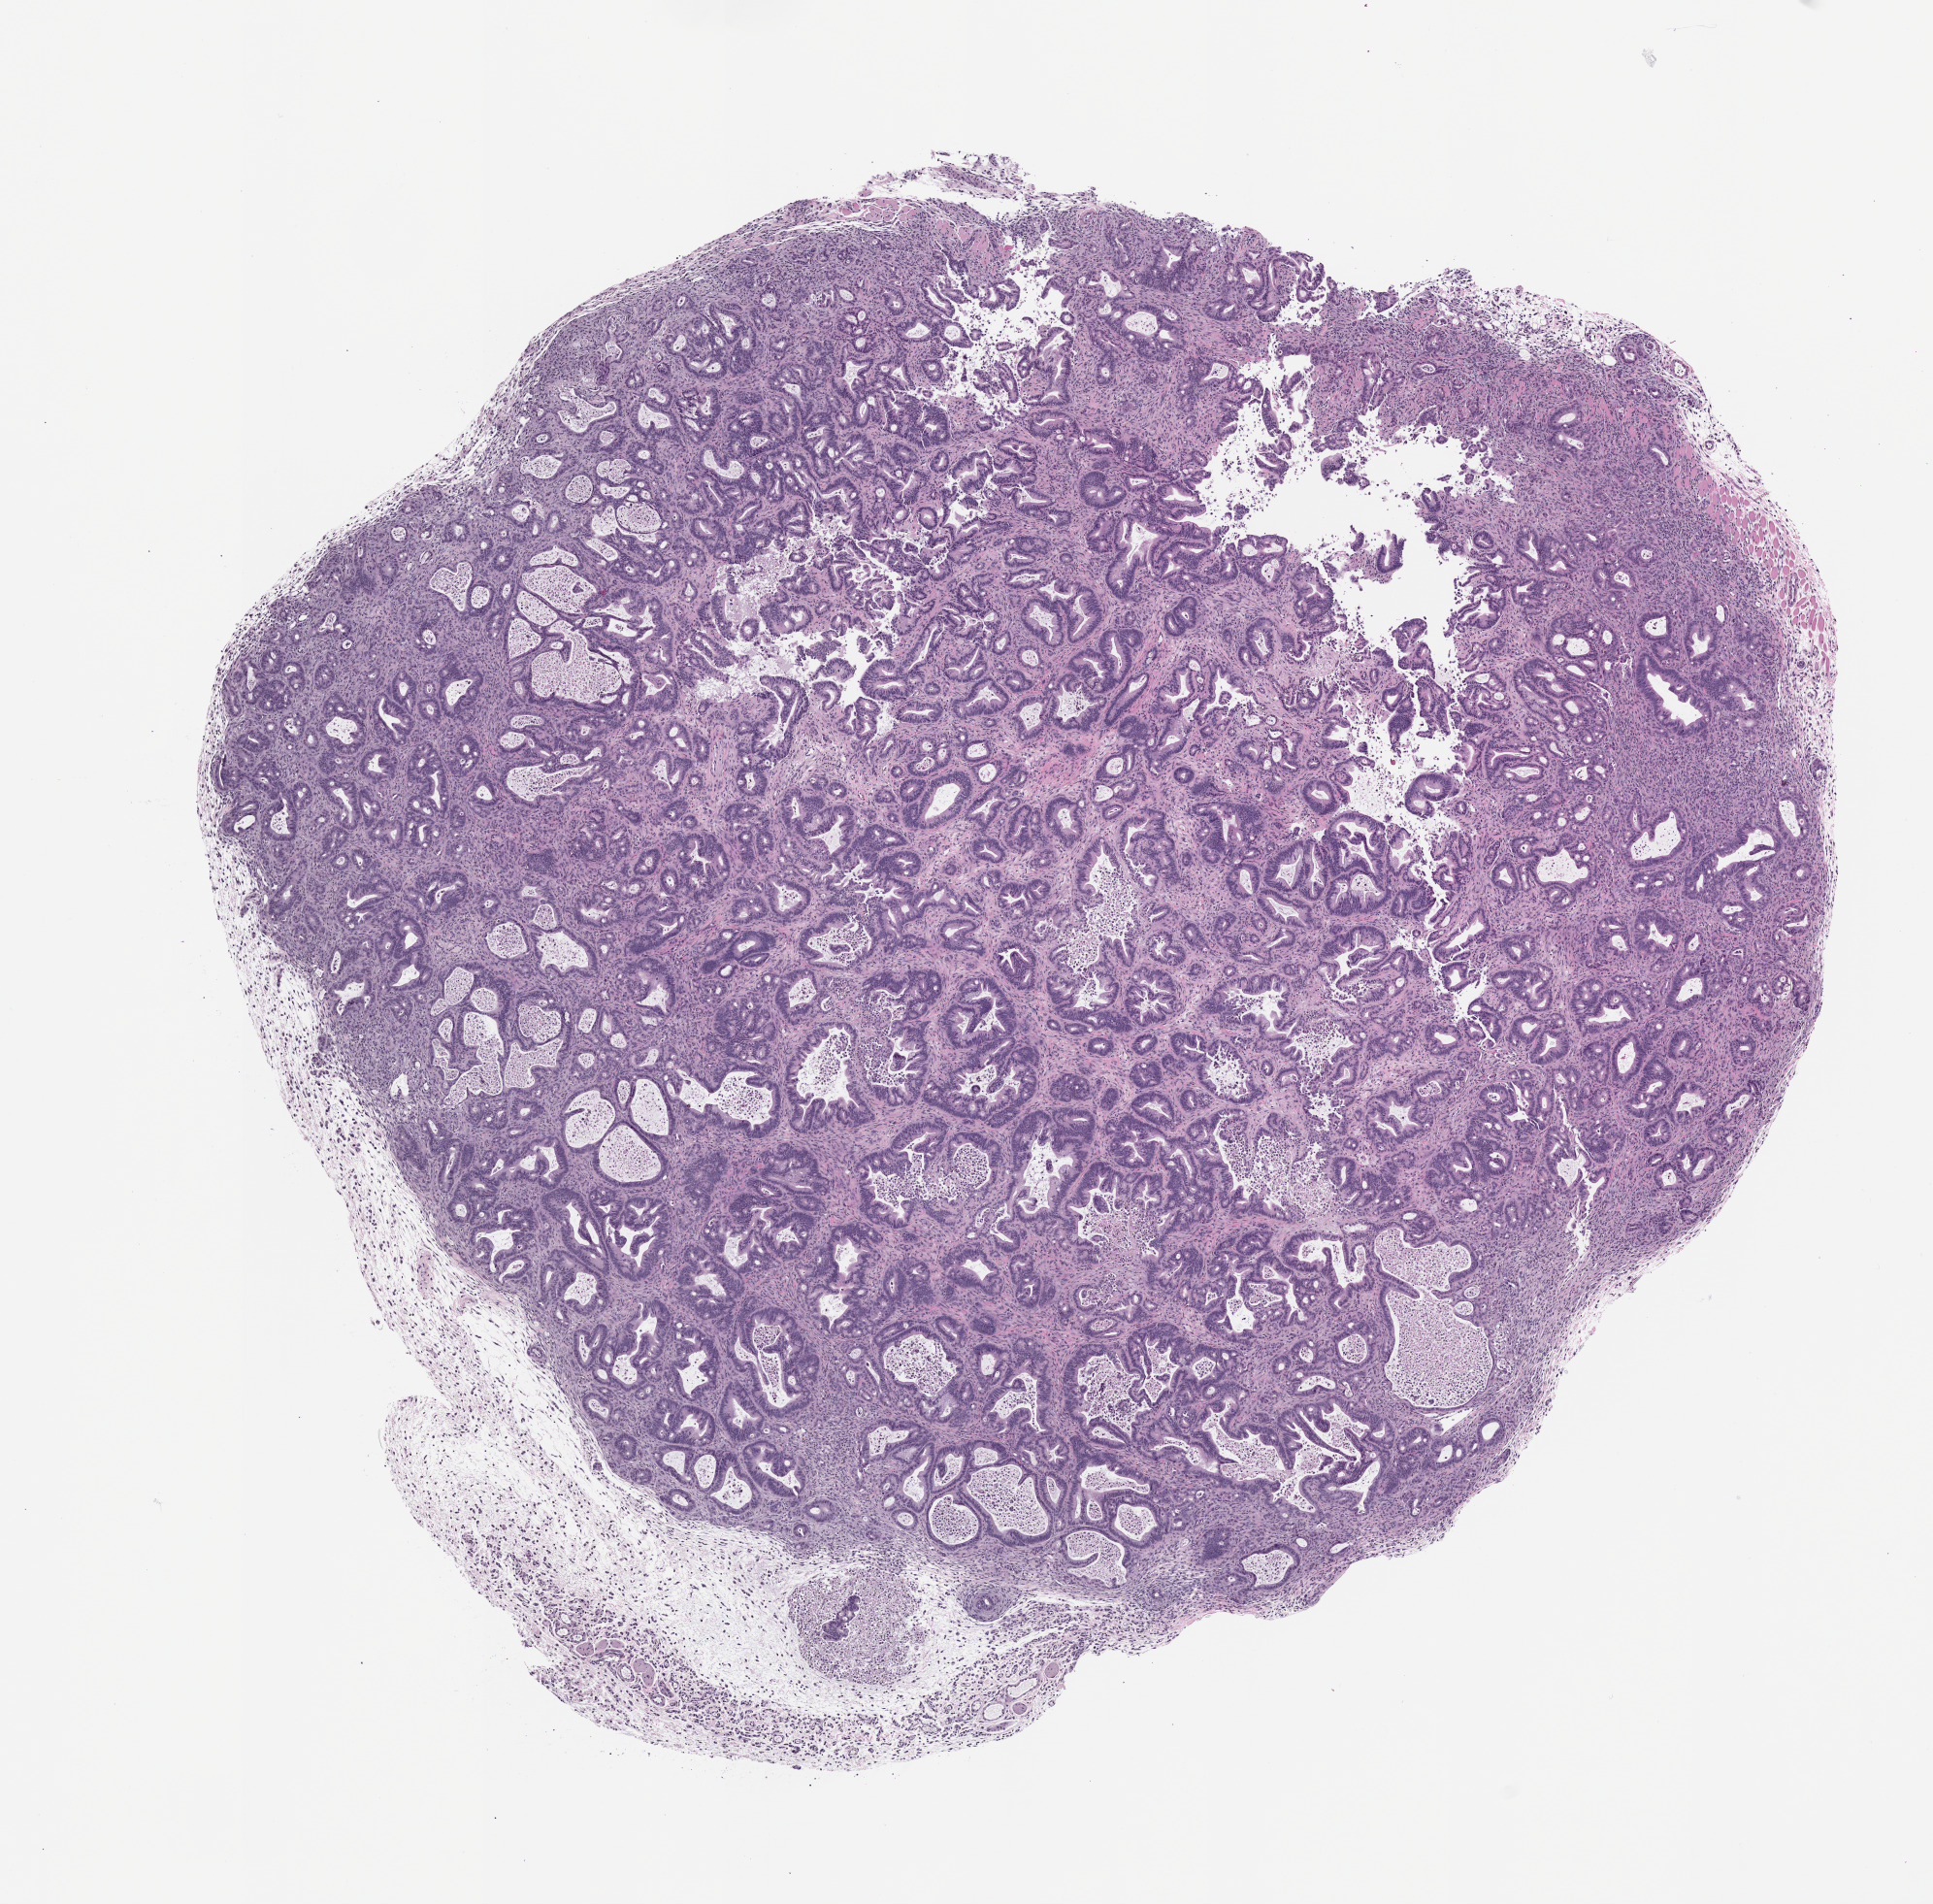
Whole-slide image, hematoxylin and eosin (H&E): patient-derived xenograft (human tumor grown in a mouse), passage 2, a low-resolution overview of the entire scanned area, about 8.0 x 7.9 mm, formalin-fixed, paraffin-embedded (FFPE) tissue, originating tumor site category: pancreas.
Originating patient diagnosis: Pancreatic Adenocarcinoma.